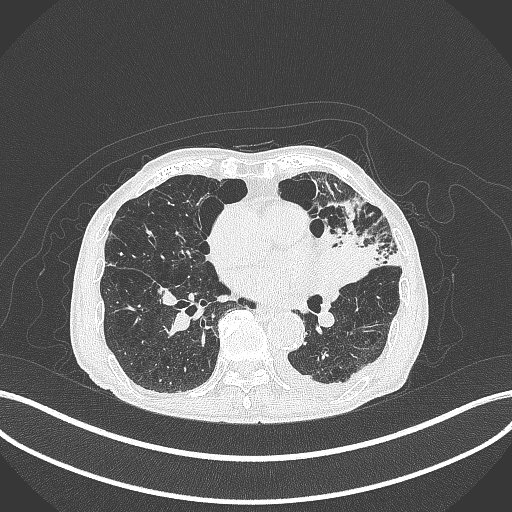
Chest CT, one axial slice; slice 175 of 385 in the series (ordered by position); lung window (W 1500 / L -600 HU); 1 mm slice thickness; 512 × 512 image matrix, field of view 400 × 400 mm. Patient: male, 90 years or older. From the clinical record (not read from this slice): clinical TNM (as recorded): T2b N1 M0.
Structures marked on this image (bounding box drawn by a radiologist):
- lung tumour (recorded histology: squamous cell carcinoma): box from (x=311, y=230) to (x=383, y=290) px